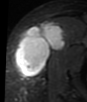
MRI of an extremity soft-tissue mass, one axial slice. Position 28 of 48 along the scan axis. STIR. MR volume resampled by the dataset authors to the PET/CT grid (not the native acquisition matrix). 3.27 mm slice thickness. 87 × 102 image matrix, field of view 85 × 100 mm. Female patient. From the clinical record (not read from this slice): histological type: synovial sarcoma; grade: intermediate; site of the primary tumour: right thigh.
Outlined on this slice (expert contour drawn on MRI and transferred to this co-registered scan by the dataset authors):
- gross tumour volume including surrounding oedema: bounding box (x1, y1, x2, y2) in pixels: (15, 22, 66, 78)
- gross tumour volume (mass): (15, 22, 66, 76)